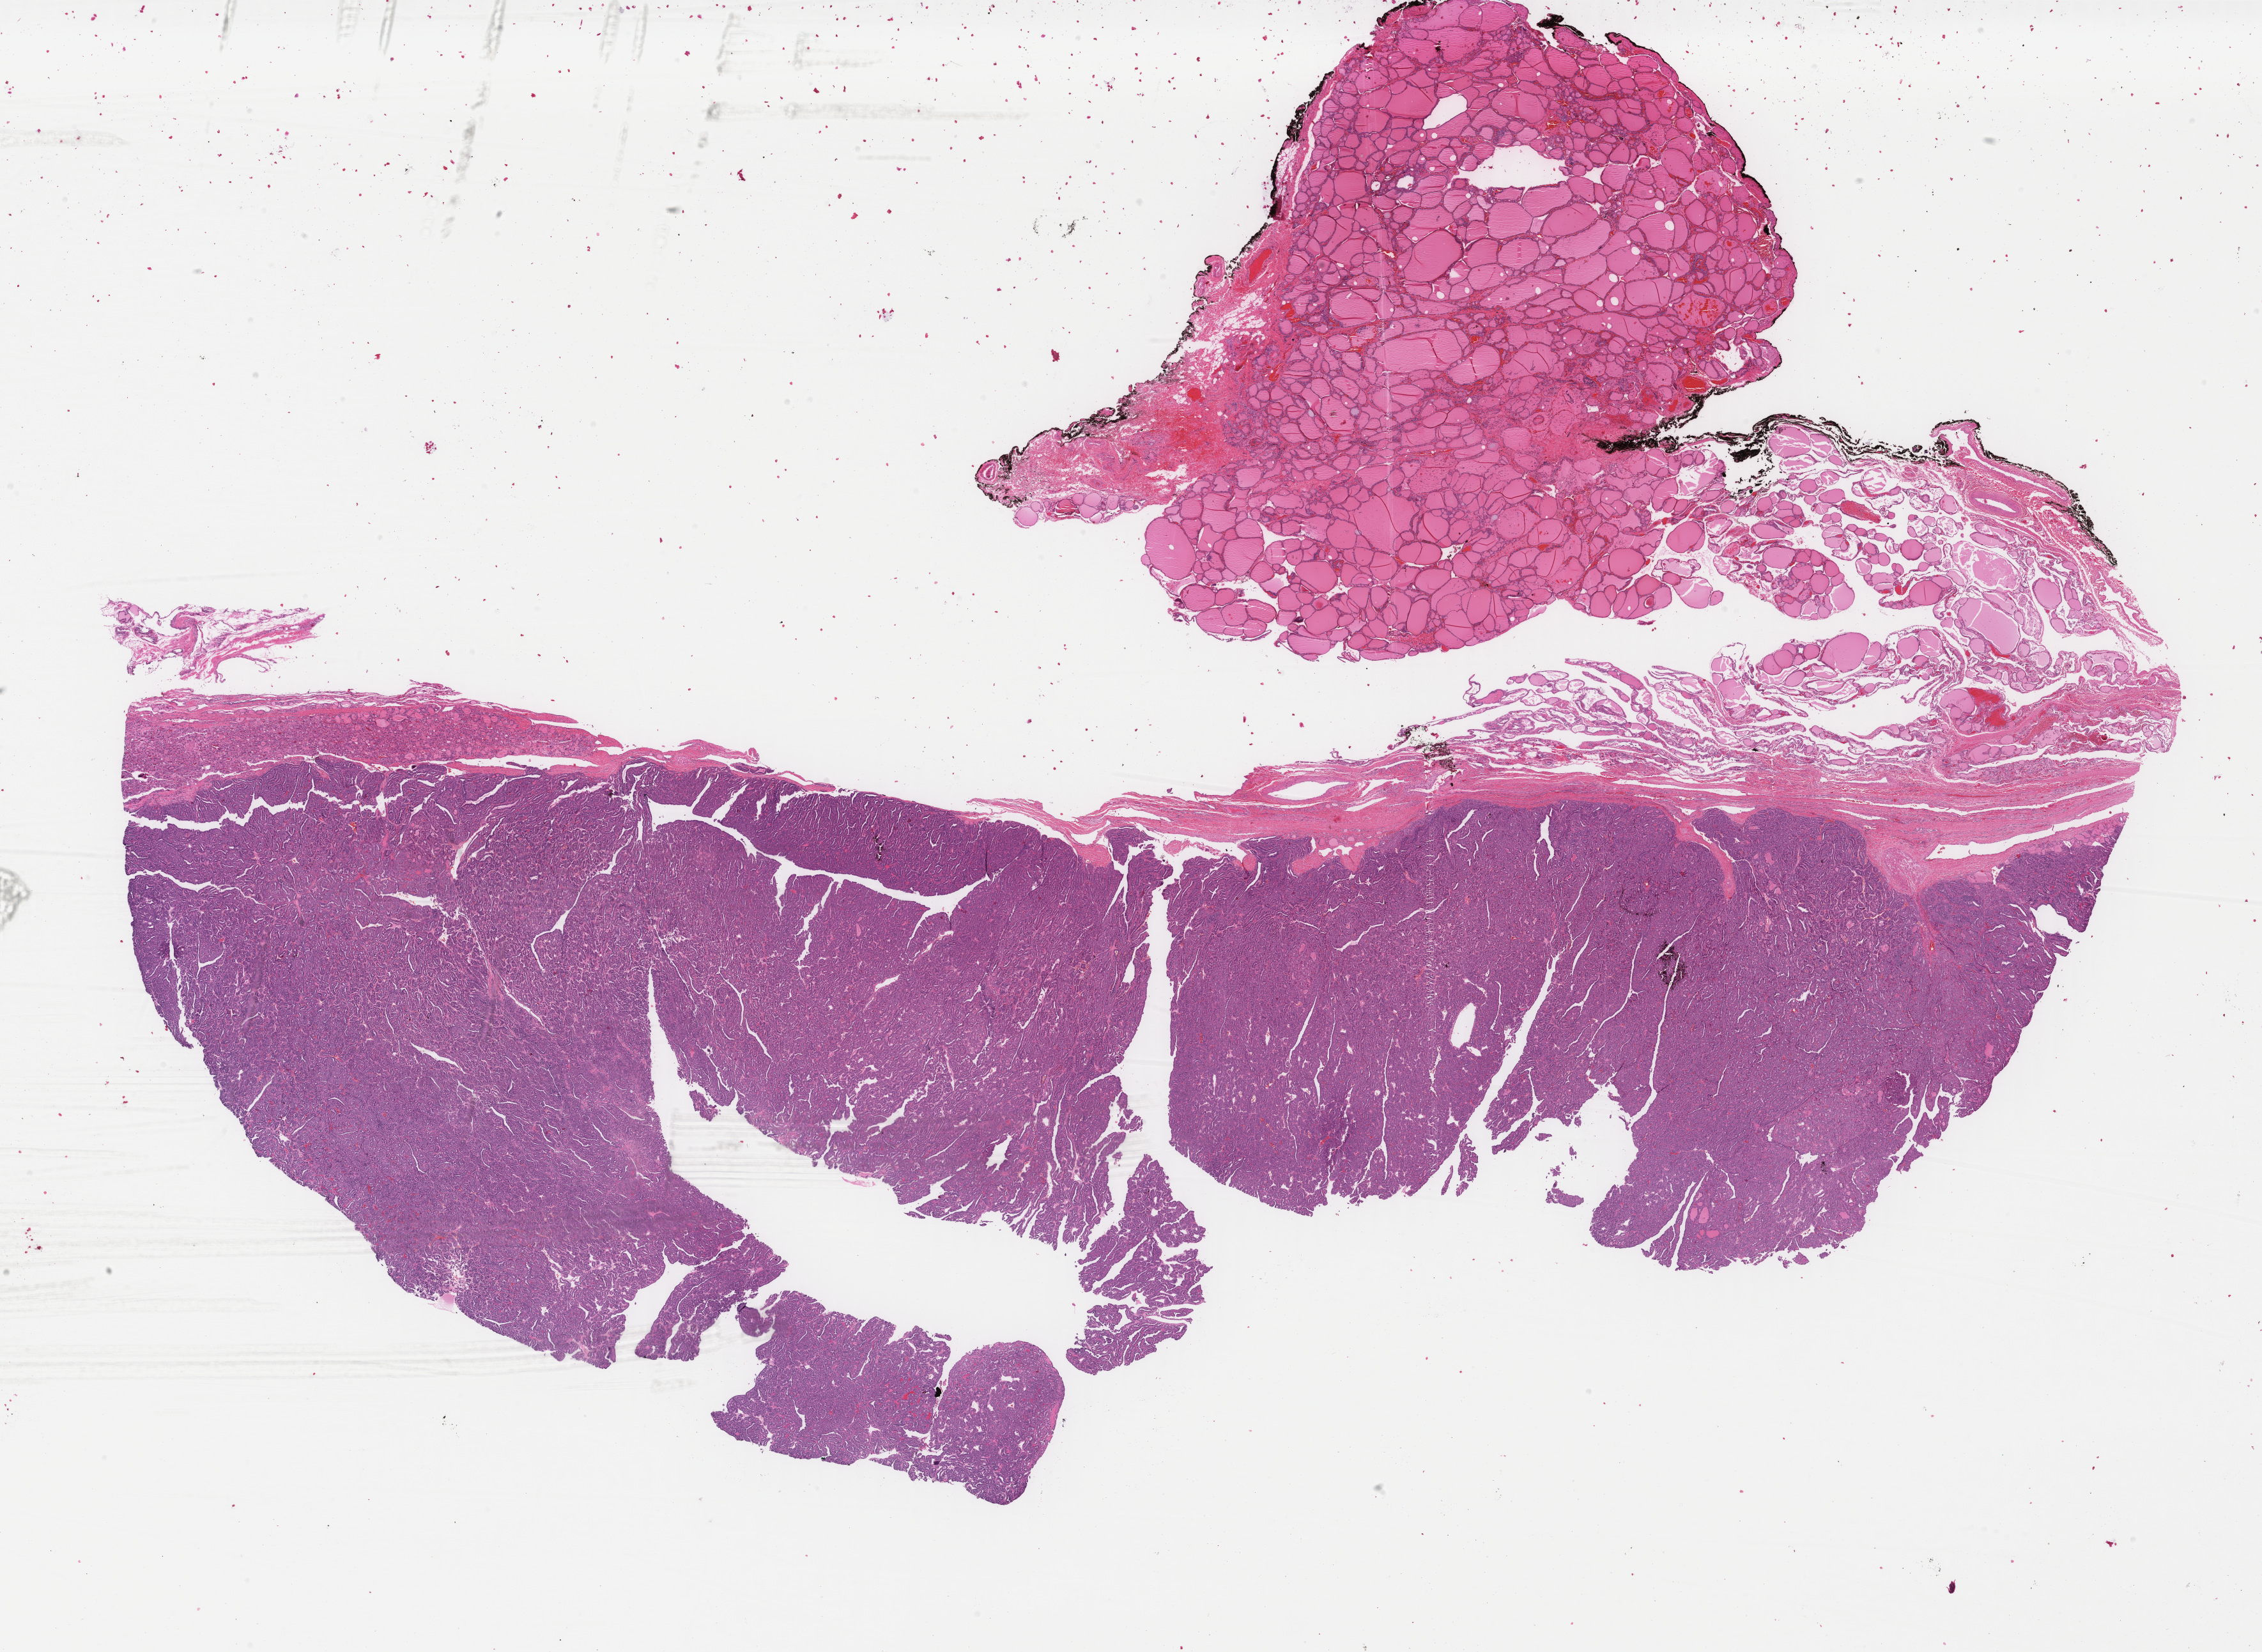
Whole-slide histology image, H&E, shown as a low-resolution overview of the whole scanned area (about 28.1 x 20.5 mm, acquisition: 40x scan), FFPE section, sample: primary tumour, thyroid. Female patient; age at initial diagnosis 35 years.
AJCC pathologic stage: I (6th edition). Diagnosis: Papillary adenocarcinoma, NOS (thyroid gland).